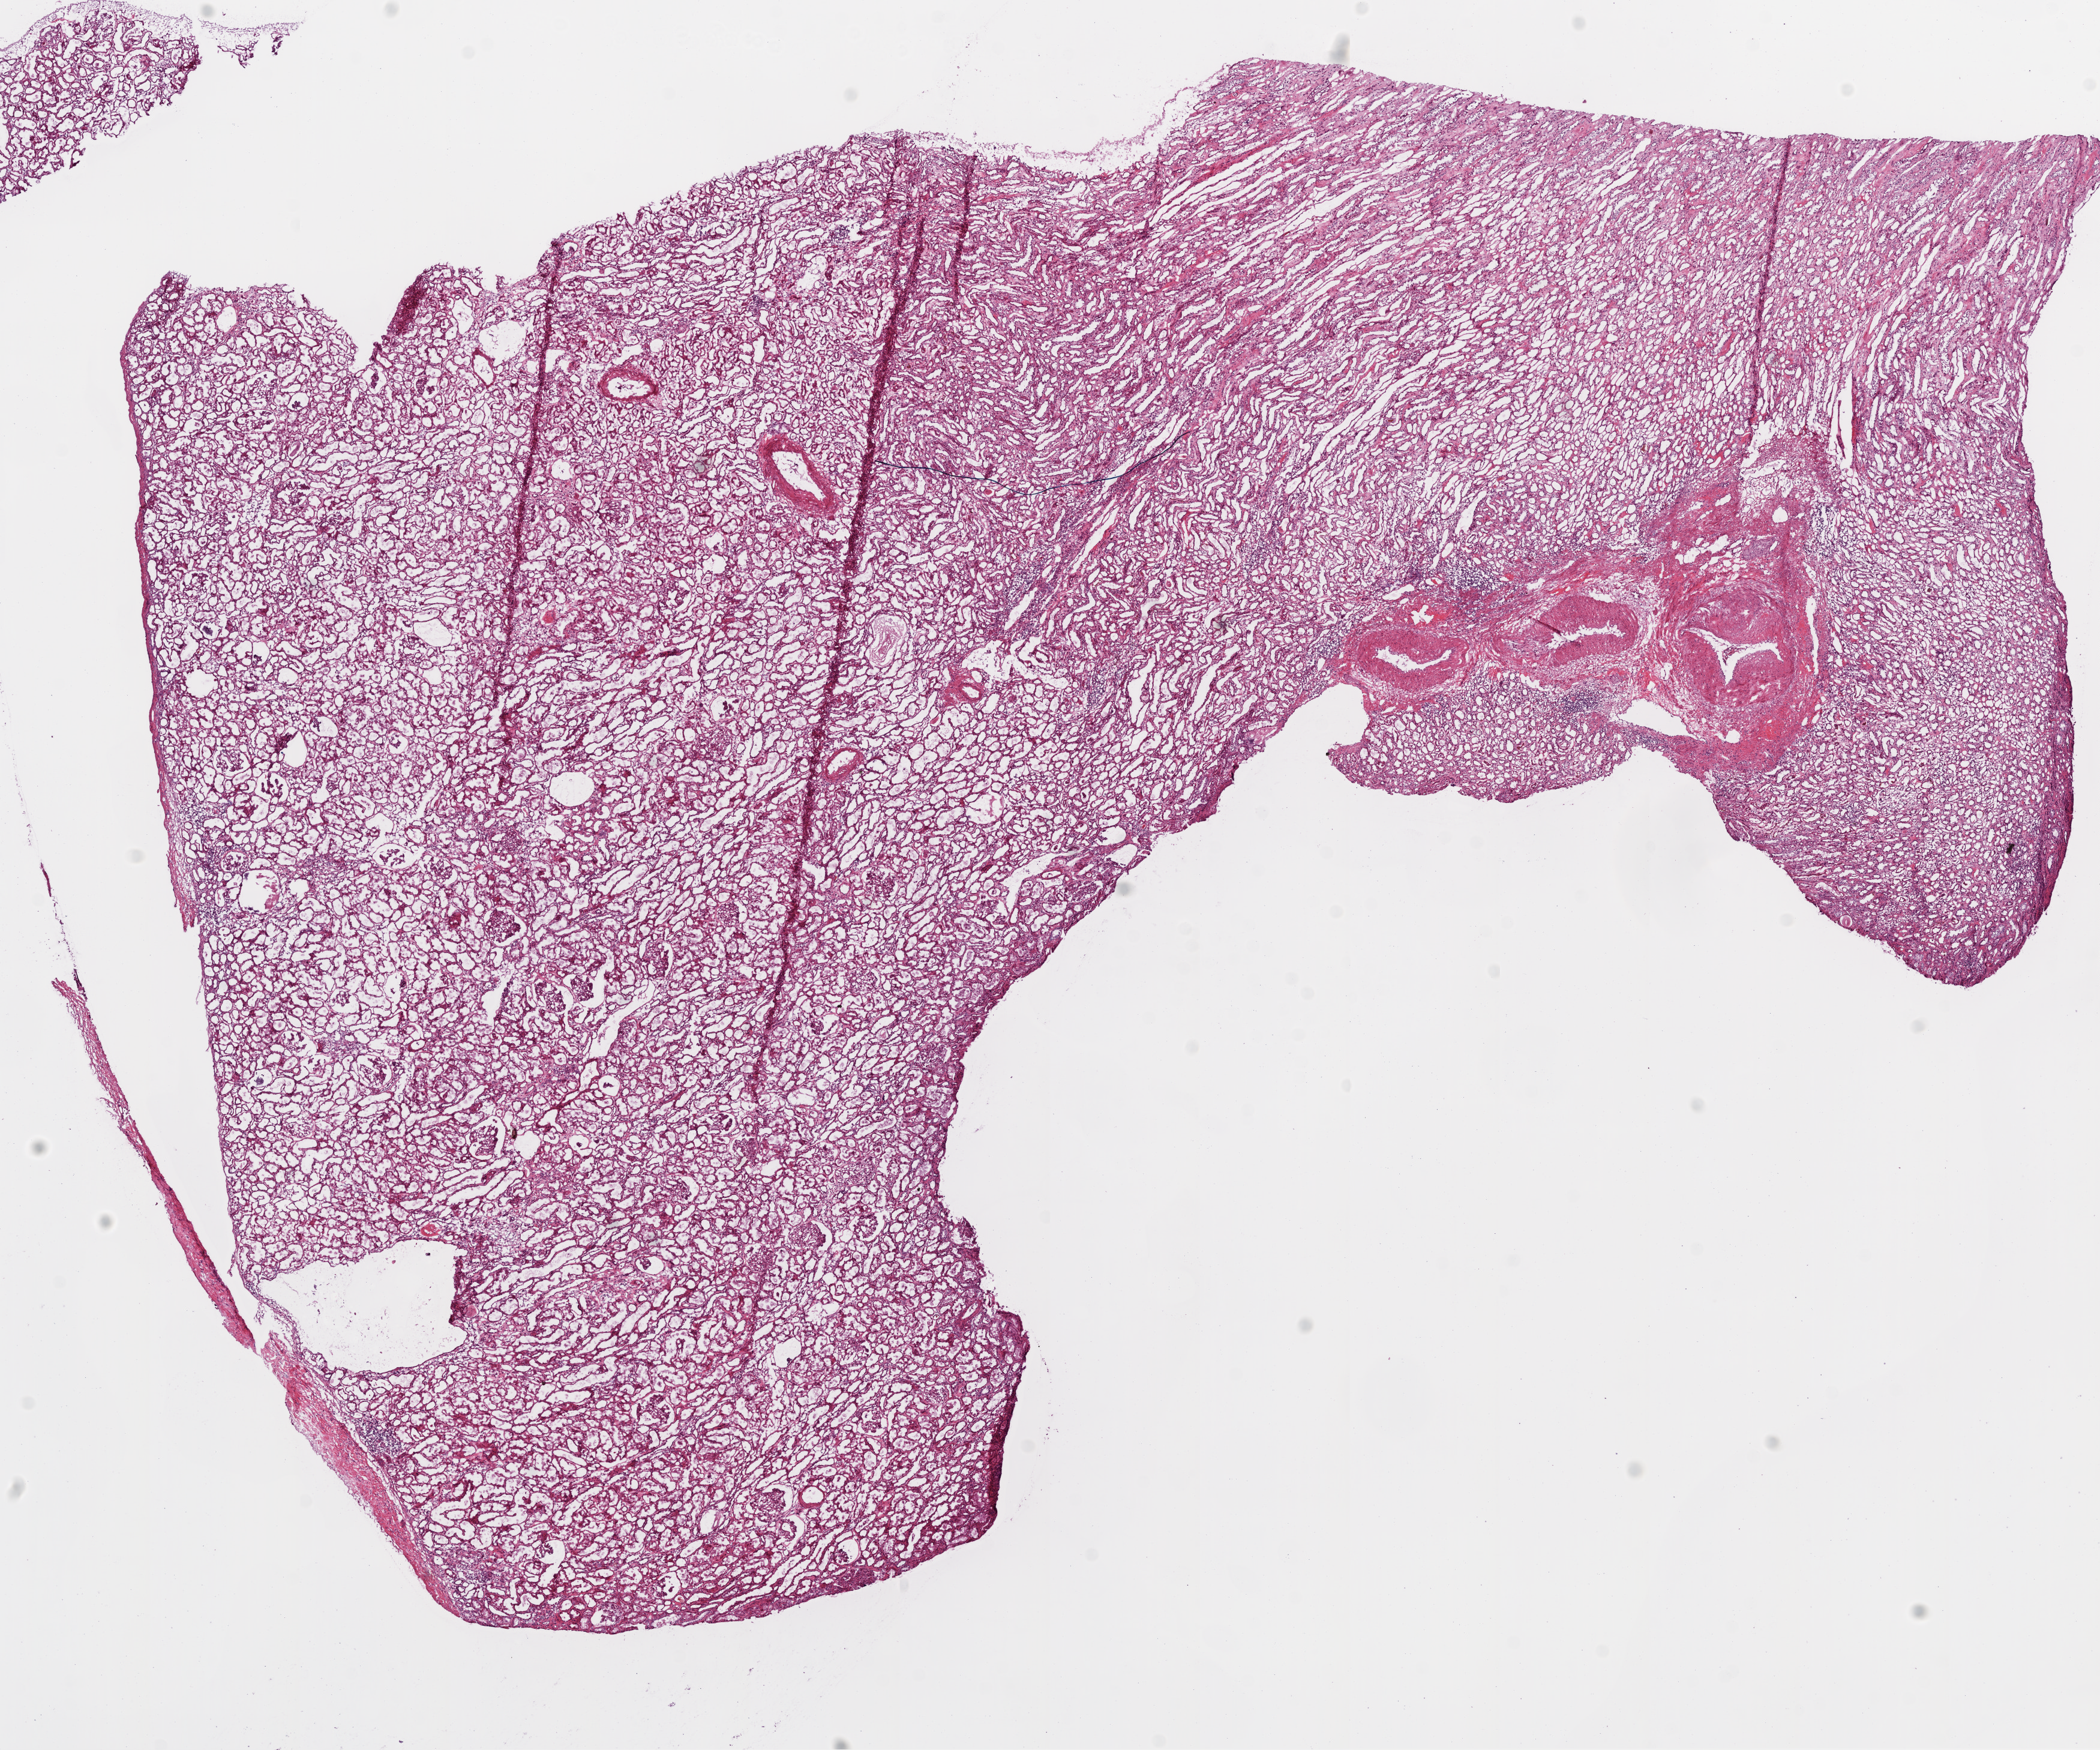
Whole-slide histology image, Hematoxylin and eosin (H&E) stained, shown as a low-resolution overview of the whole scanned area (about 14.0 x 11.7 mm). Frozen section from the bottom of the tissue portion. Sample: solid tissue normal (non-tumour tissue), kidney. Female patient; age at initial diagnosis 76 years.
This section: solid tissue normal (non-tumour) sample from the same patient. Patient diagnosis: Clear cell adenocarcinoma, NOS.